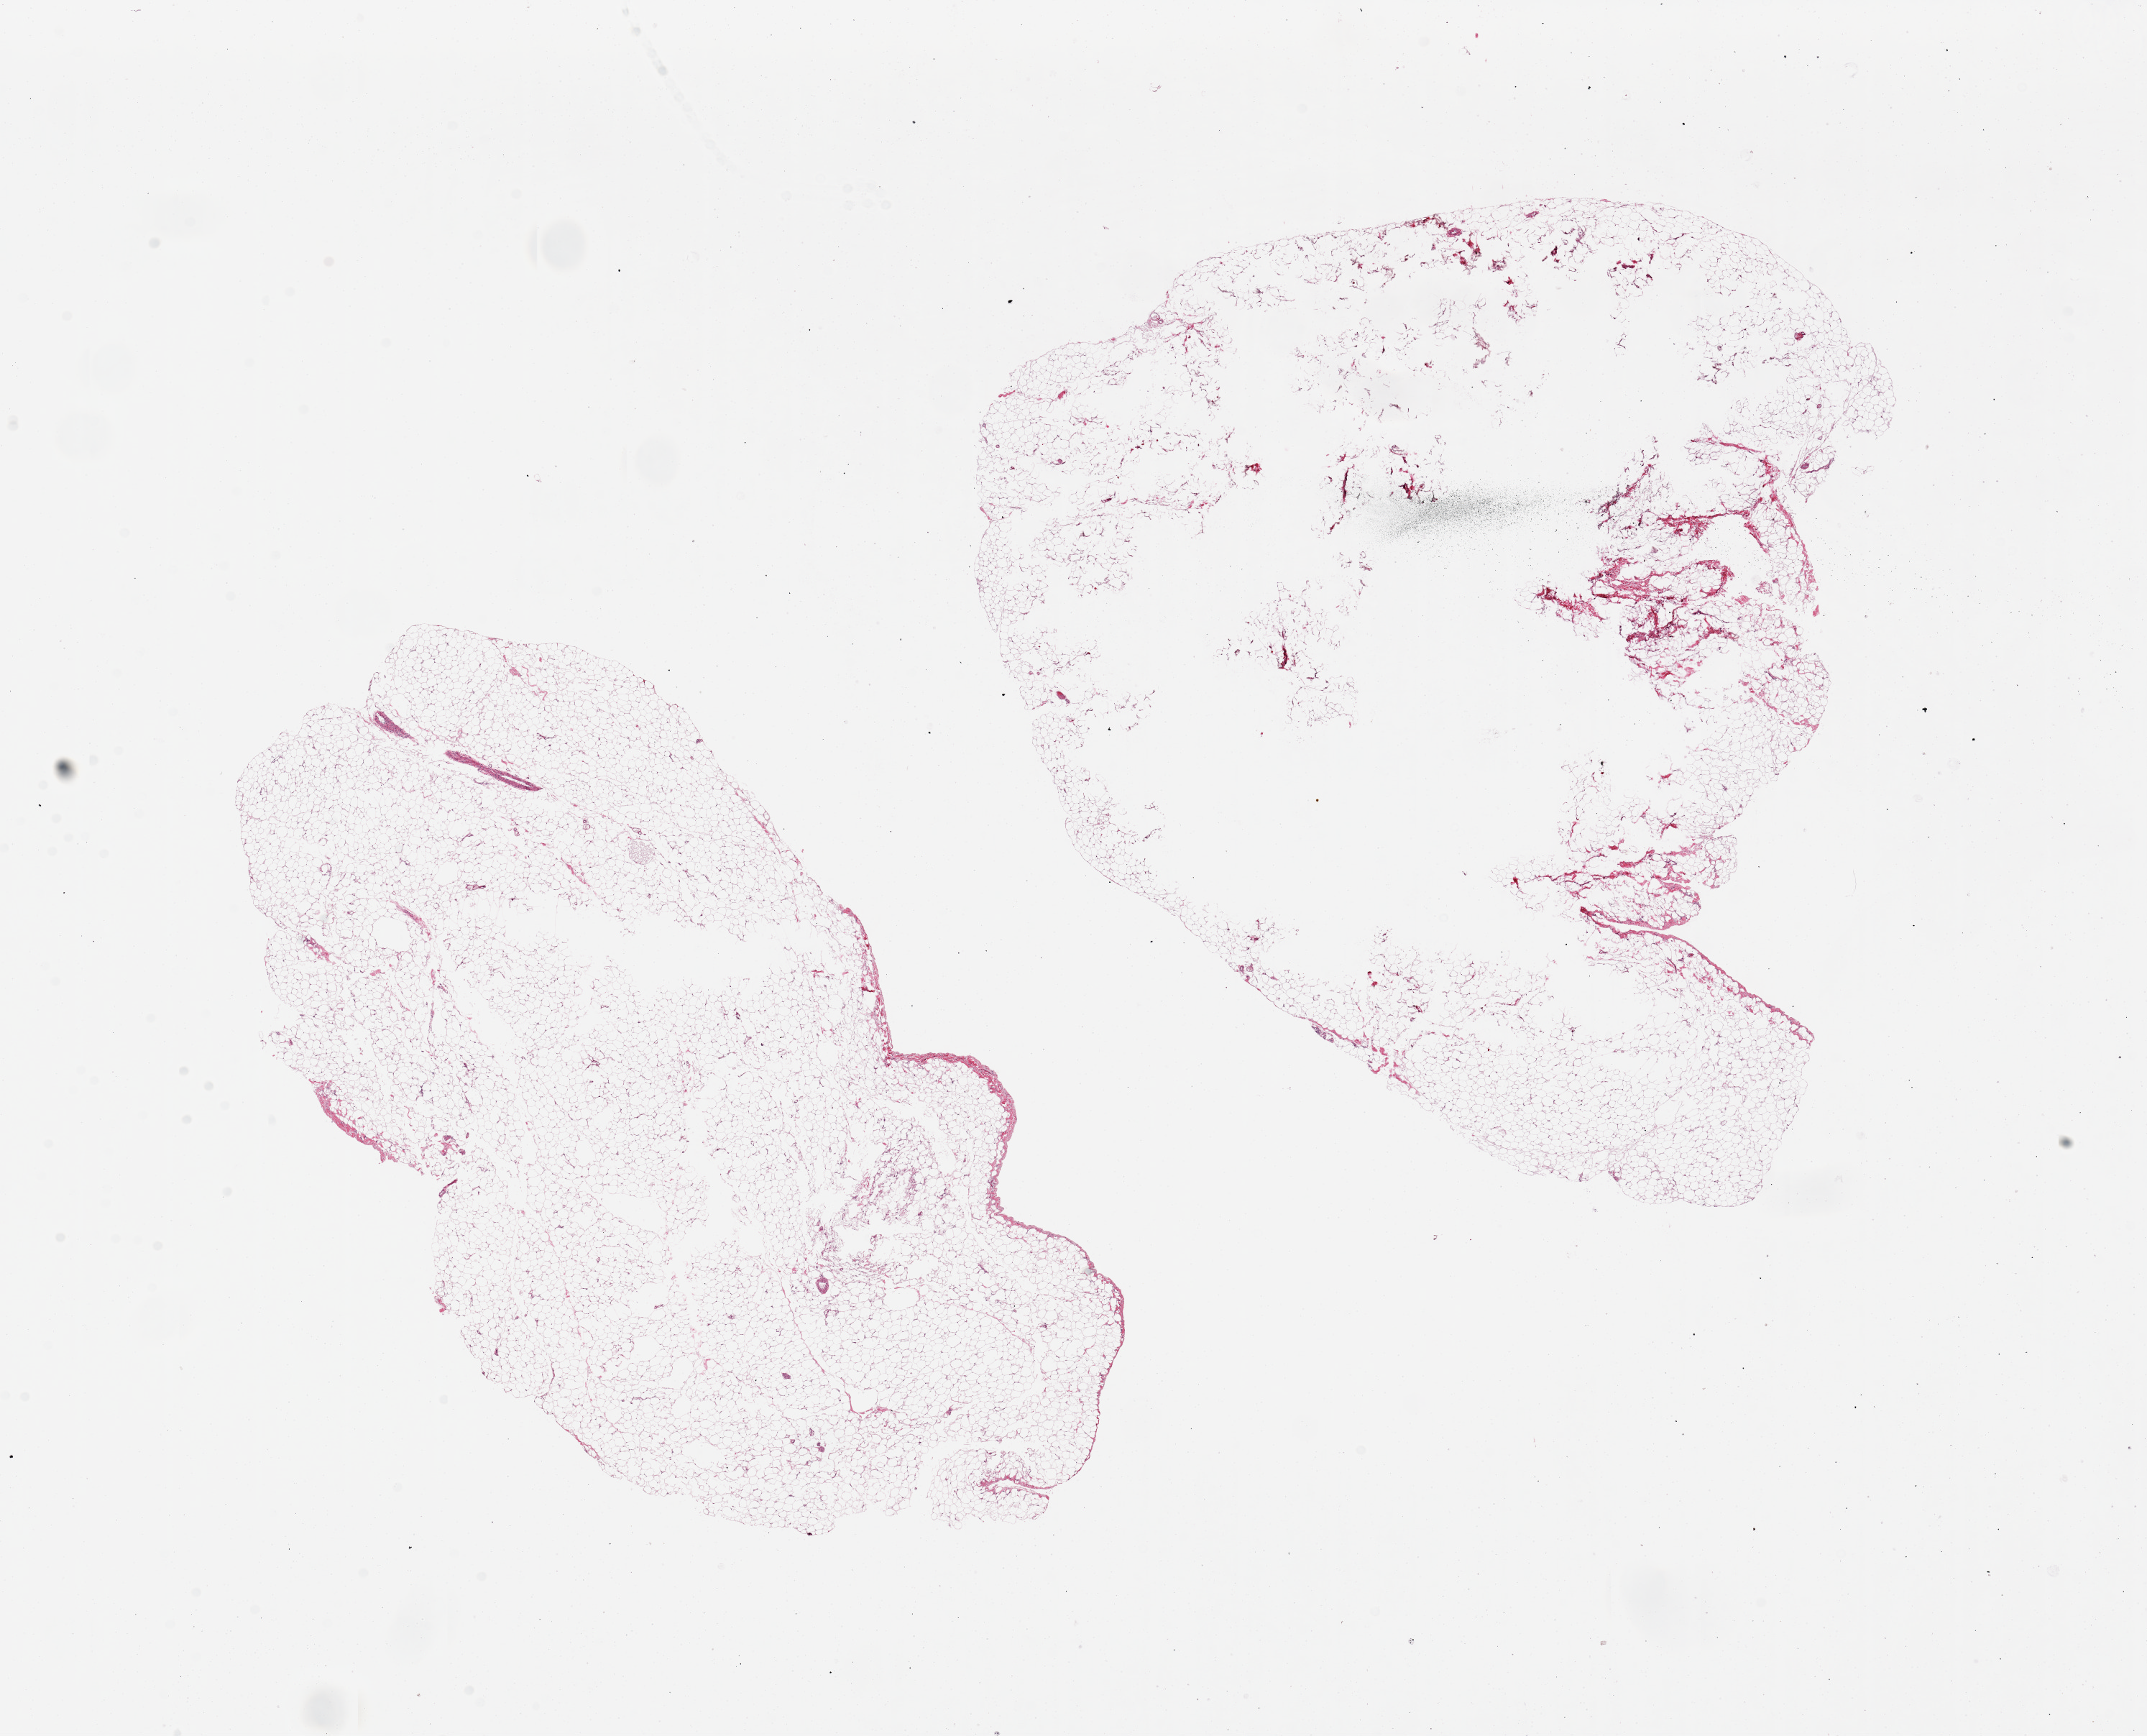
Whole-slide image, haematoxylin and eosin stain, a low-resolution overview of the entire scanned area, about 23.6 x 19.1 mm. PAXgene-fixed, paraffin-embedded tissue. Target tissue: omentum. Donor tissue sample. Donor: female.
Reviewer comment on this tissue sample: 2 pieces, 12x6 & 12x10mm. 1 well fixed, other with large central holes.